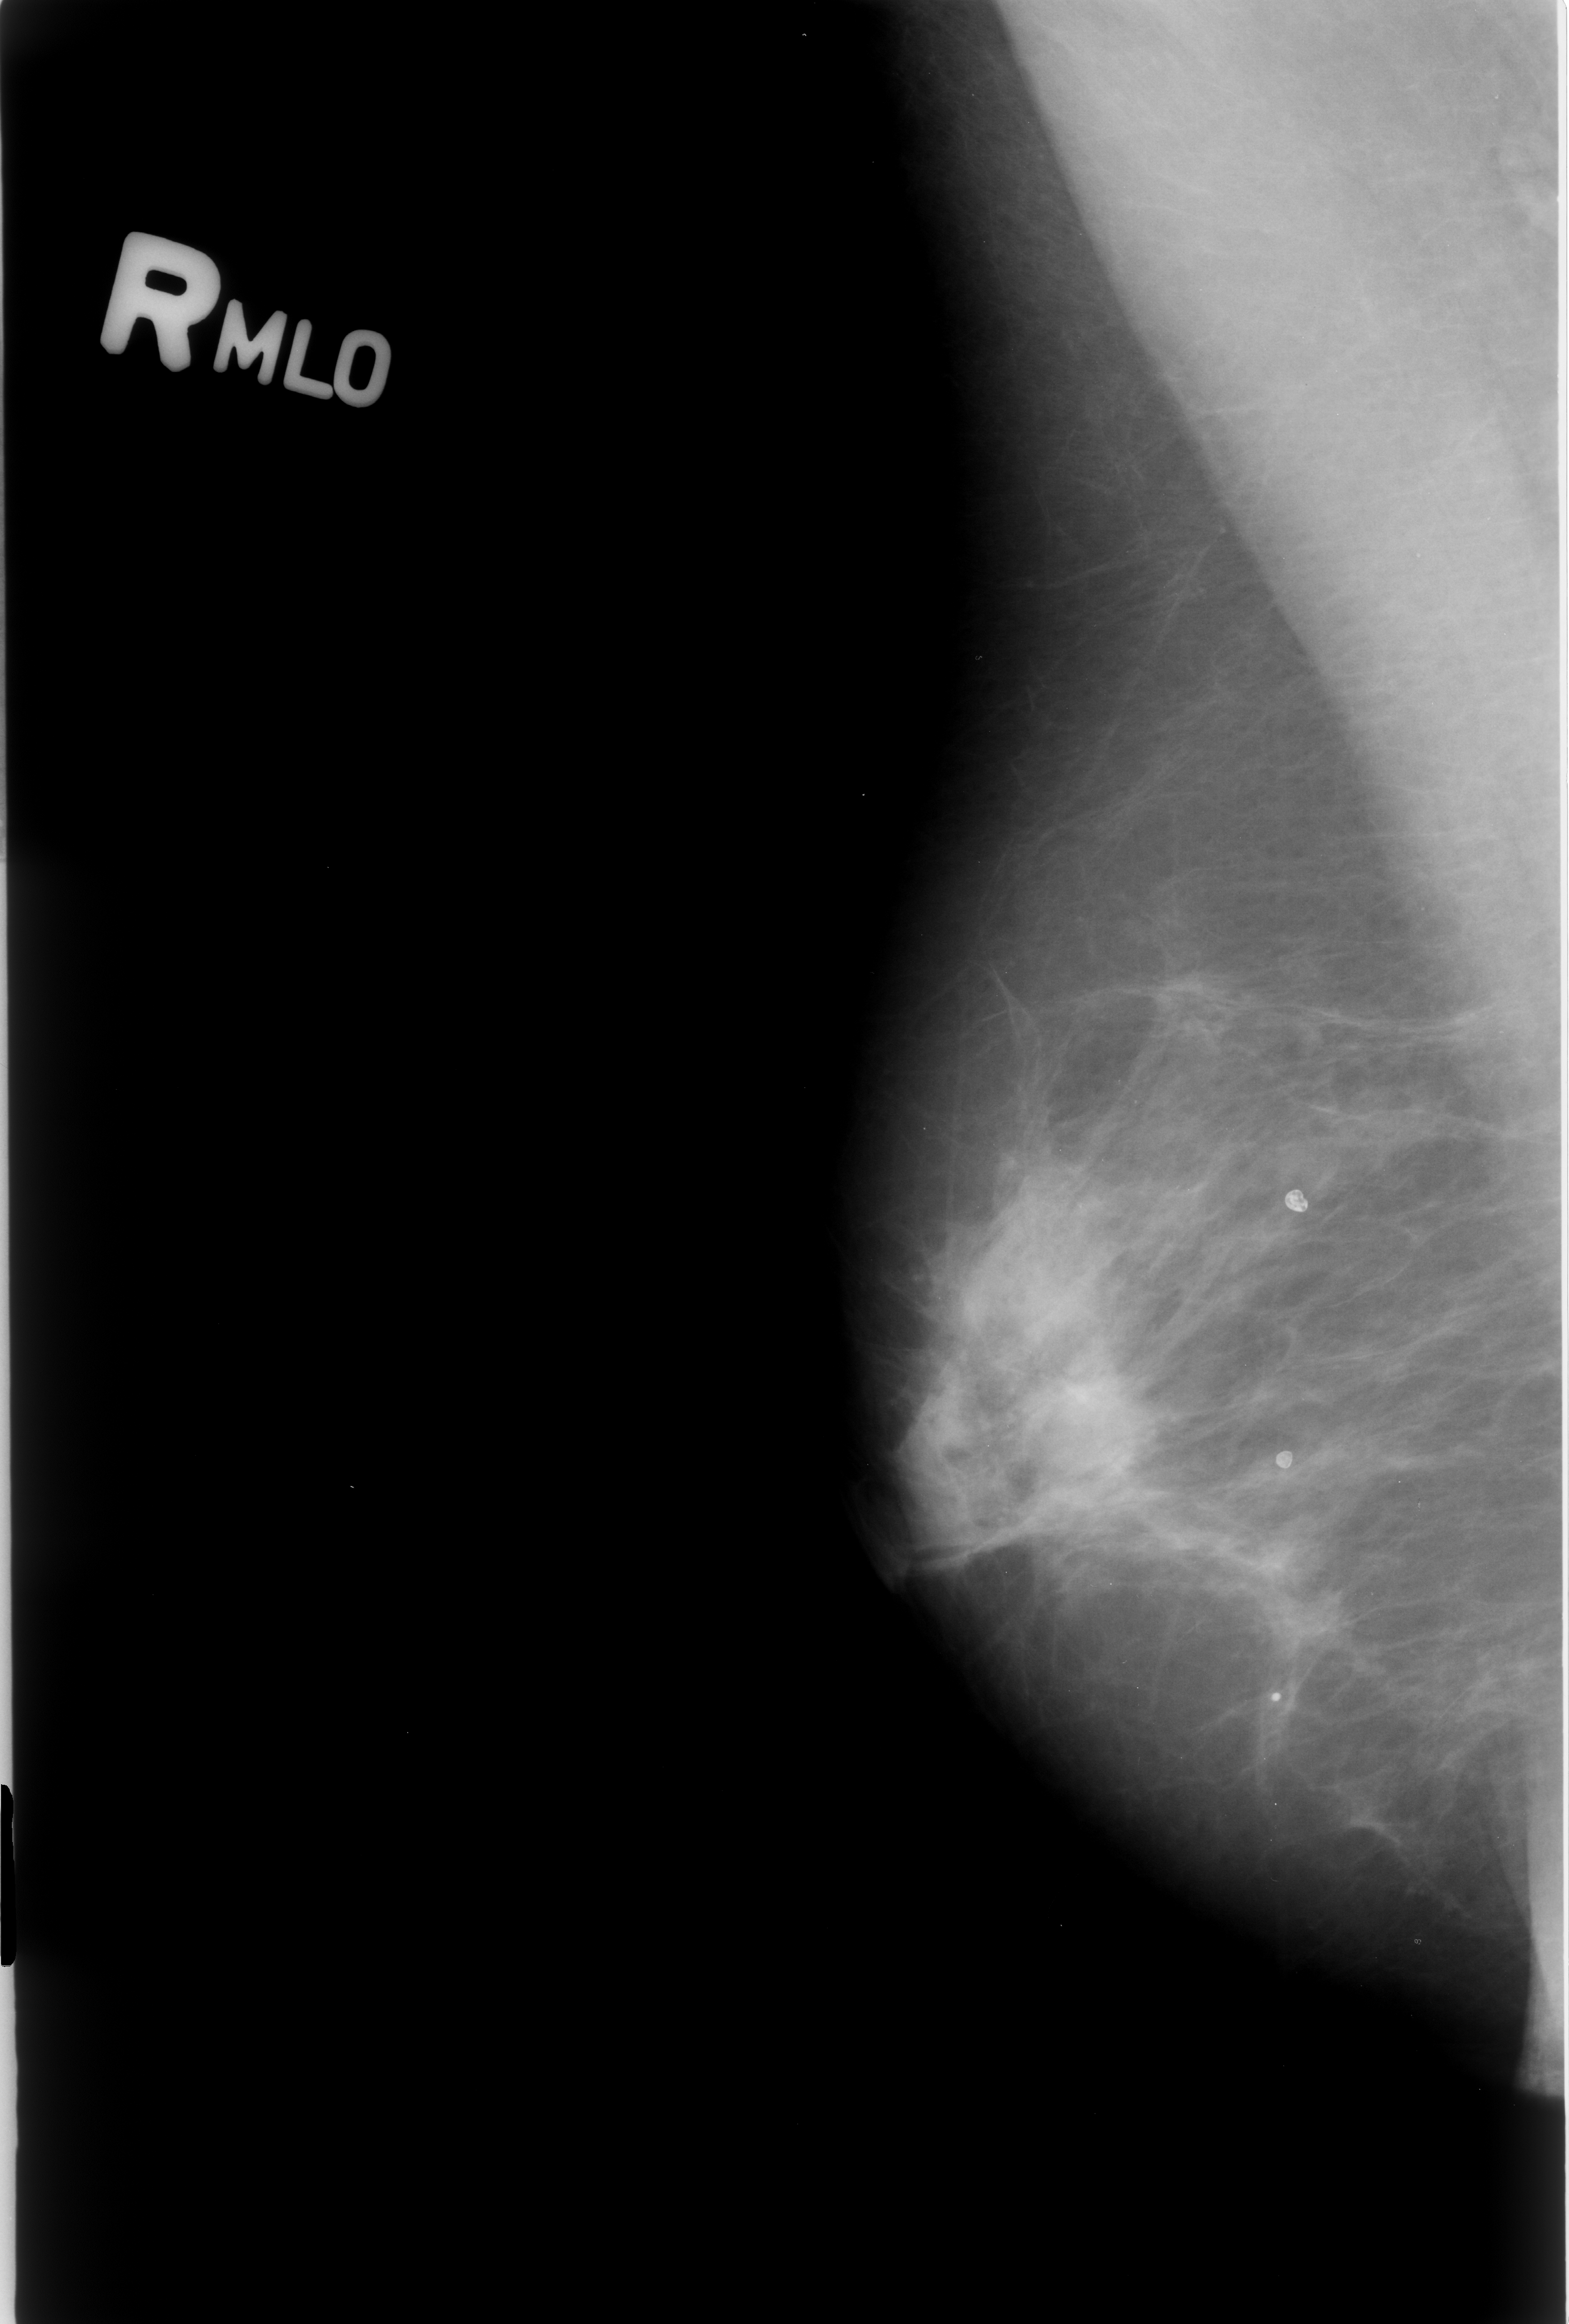
Mammogram (digitized film); right breast; mediolateral oblique (MLO) view; BI-RADS breast density category 3 (scale 1–4).
- Marked findings (only marked abnormalities are described; nothing is implied about the rest of the image): mass, shape irregular, margins obscured / ill defined; BI-RADS assessment category 3; pathology result (as recorded, not read from the image): malignant.